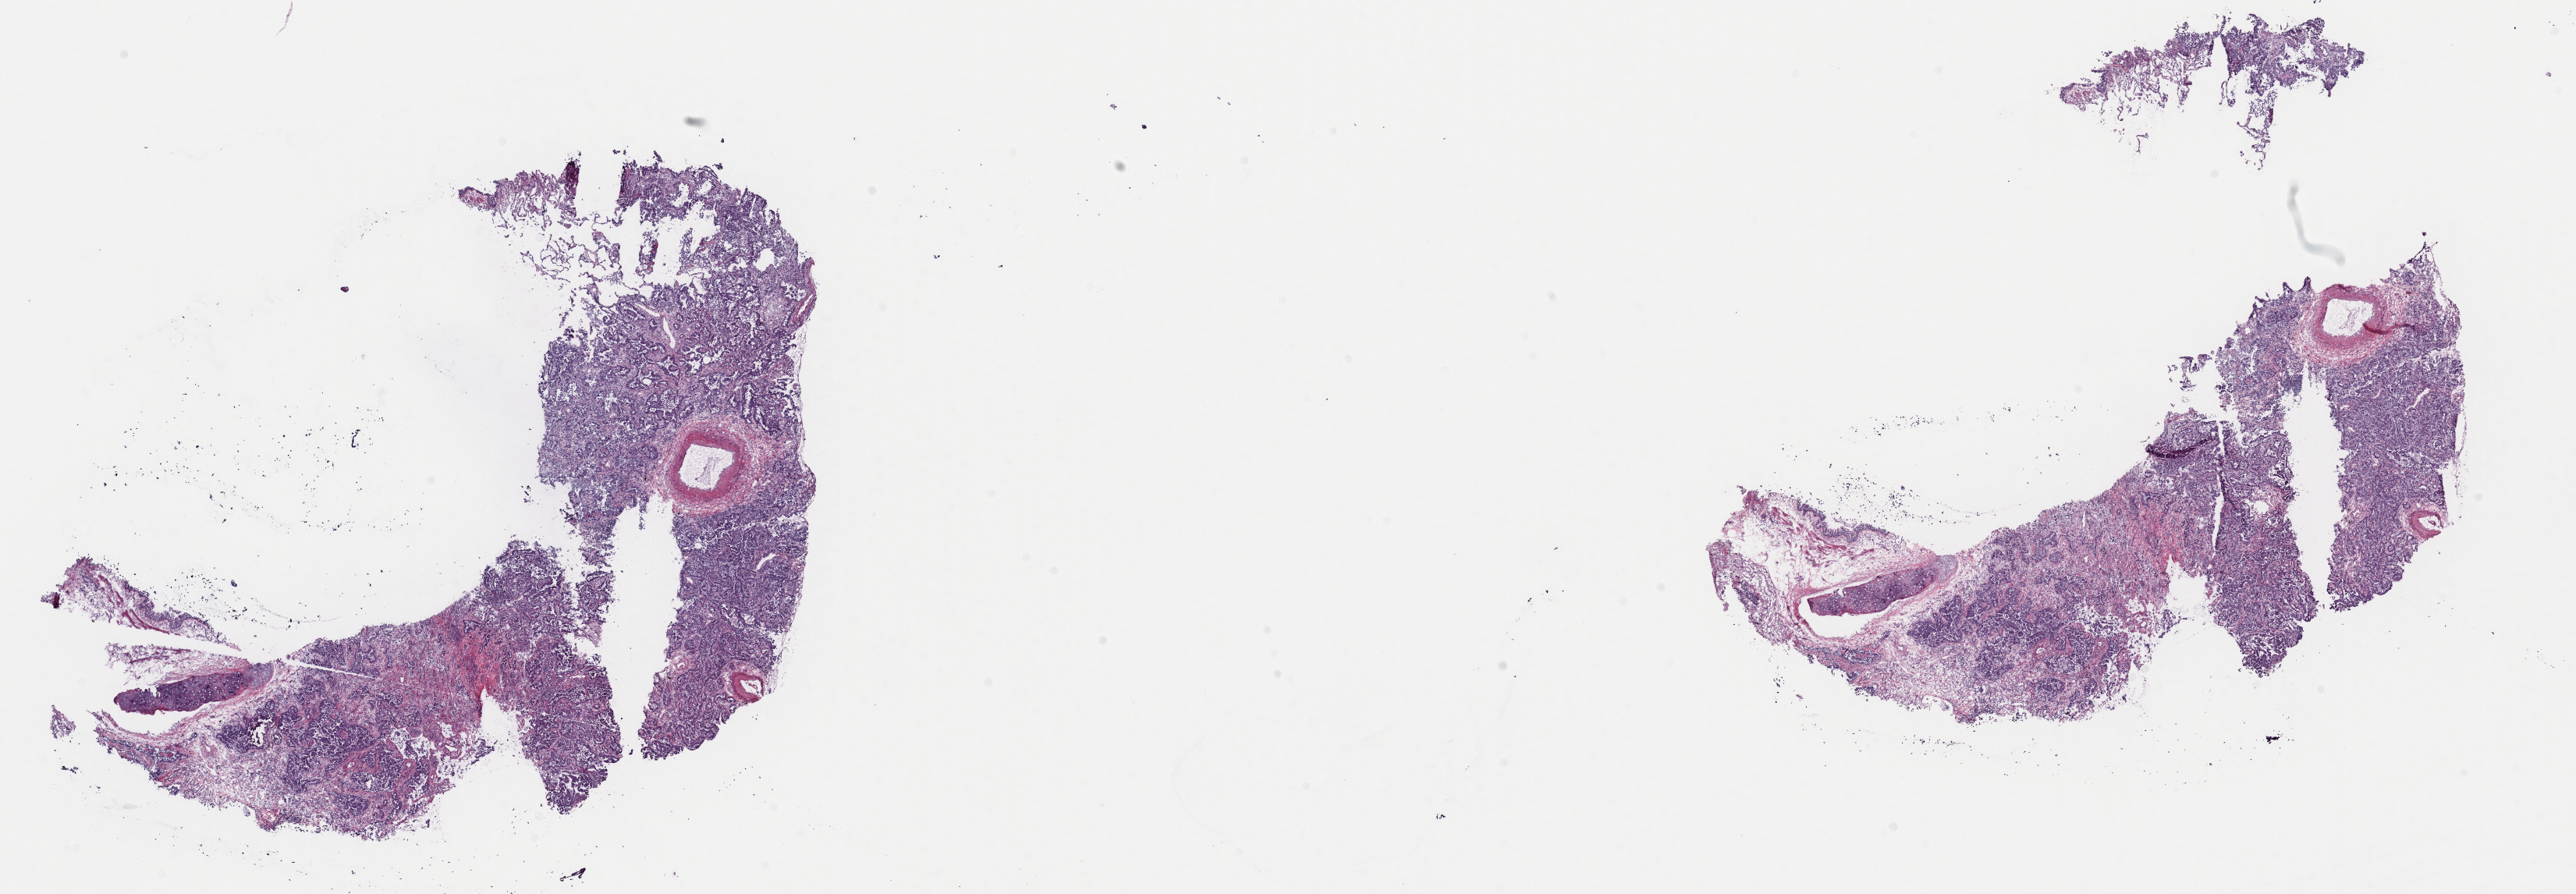
Hematoxylin and eosin (H&E) stained whole-slide image, low-resolution overview of the scanned area, about 26.1 x 9.1 mm. Frozen section from the top of the tissue portion. Lung, primary tumour sample. Patient: female, age at initial diagnosis 67 years. Composition of this section per pathologist review: tumour cells 75%, tumour nuclei 75%, normal cells 0%, stromal cells 20%, necrosis 5%. Inflammatory infiltration, as recorded: lymphocyte infiltration 20%, monocyte infiltration 20%, neutrophil infiltration 40%.
- TNM: T1b NX M0
- AJCC pathologic stage: IA
- histologic diagnosis: Adenocarcinoma, NOS (upper lobe, lung)